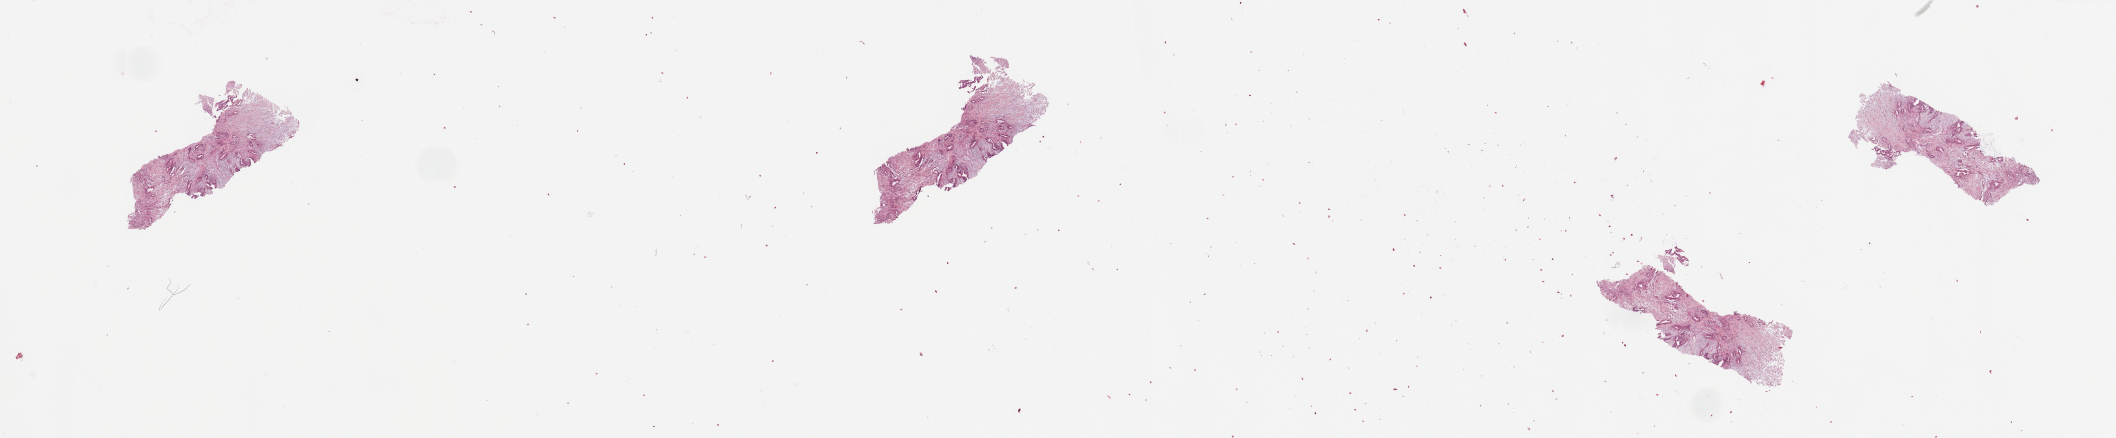
H&E-stained whole-slide image — low-resolution overview of the scanned area, about 33.5 x 6.9 mm (from a 20x scan). Tumour tissue sample, sampled site: pancreas. Patient: female, age 53 years. Histologic grade: G2 (moderately differentiated). Composition of this section per pathologist review: tumour nuclei 25%, necrosis 0%.
* primary tumour site (as recorded): head
* AJCC pathologic stage: III
* histologic diagnosis: Infiltrating duct carcinoma, NOS